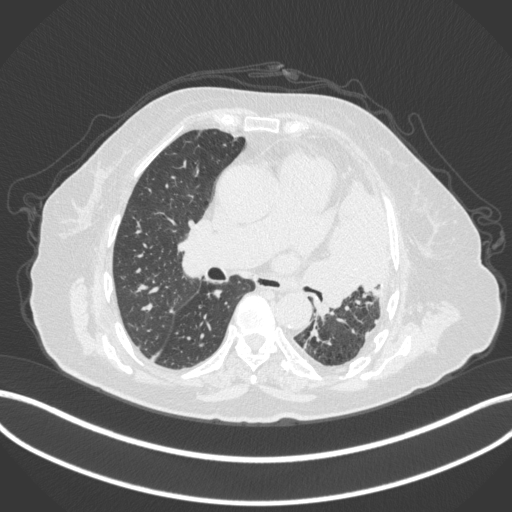
Chest CT, one axial slice; position 207 of 399 along the scan axis; lung window (W 1500 / L -600 HU); 512 × 512 image matrix, field of view 400 × 400 mm. Patient: female, 75 years. Case-level facts recorded for this patient, not image findings: clinical TNM (as recorded): T3 N3 M1.
Structures marked on this image (bounding box drawn by a radiologist):
- lung tumour (recorded histology: adenocarcinoma): box from (x=308, y=175) to (x=390, y=315) px